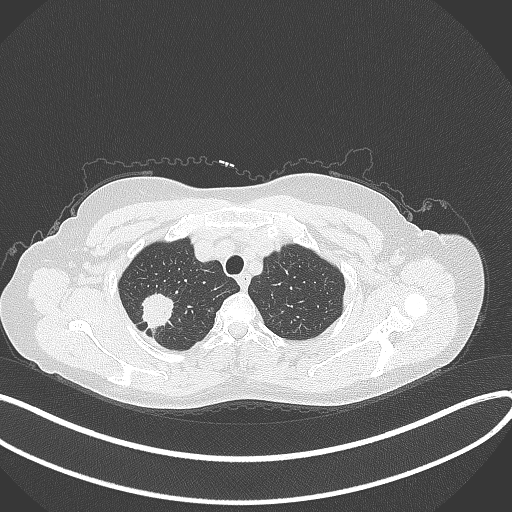
Chest CT, one axial slice. Slice 310 of 337 in the series (ordered by position). Reconstruction kernel B70f. Lung window (W 1500 / L -600 HU). 1 mm slice thickness. 512 × 512 image matrix, field of view 400 × 400 mm. Female patient, age 50 years. Case-level facts recorded for this patient, not image findings: clinical TNM (as recorded): T1c N0 M0; histopathological grade: G2-3.
Outlined on this slice (bounding box drawn by a radiologist):
- lung tumour (recorded histology: adenocarcinoma): bounding box <132,288,178,336> (left, top, right, bottom; pixels)